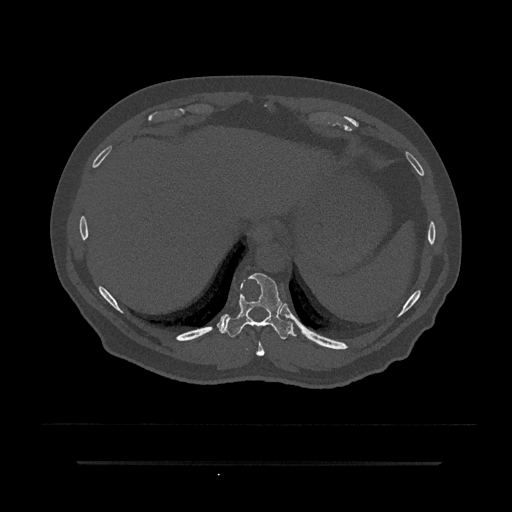
CT including the spine, one axial slice; position 334 of 797 along the scan axis; reconstruction kernel Br40s/3; 120 kVp; bone window (W 1800 / L 400 HU); 0.5 mm slice thickness; 512 × 512 image matrix, field of view 464 × 464 mm. Patient: male, 59 years. From the clinical record (not read from this slice): primary cancer: bile ducts; vertebrae with lytic lesions (as recorded): T10.
Structures marked on this image (semi-automatic segmentation, software-assisted and operator-edited):
- T10 vertebra: box from (x=223, y=273) to (x=296, y=339) px
- T9 vertebra: (x=256, y=341)–(x=265, y=356)